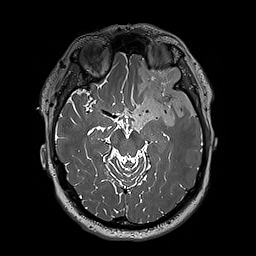
Brain MRI from a brain-tumour surgery series, one axial slice; slice 128 of 192 in the series (ordered by position); 1 mm slice thickness; 256 × 256 image matrix, field of view 250 × 250 mm. From the clinical record (not read from this slice): histopathology: Oligodendroglioma; WHO grade: 3; IDH mutation: yes.
Annotated regions visible in this slice (expert manual segmentation):
- tumour: bounding box [x1, y1, x2, y2] px = [124, 61, 197, 131]